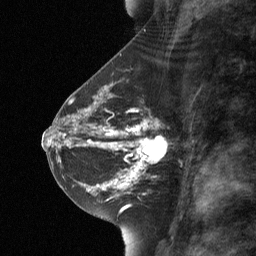
Breast MRI (dynamic contrast-enhanced), one sagittal slice; slice 32 of 64 in the series (ordered by position); dynamic contrast-enhanced study with each time point stored as its own series, time point 2 of 3 at this slice position (early post-contrast, ordered by acquisition time); 1.5 T; TE 4.8 ms, TR 27 ms; 2 mm slice thickness; 256 × 256 image matrix, field of view 180 × 180 mm. Patient: female, 42 years. Case-level facts recorded for this patient, not image findings: setting: breast cancer imaged before/during neoadjuvant chemotherapy; receptor status: triple-negative.
Outlined on this slice (semi-automatic segmentation, software-assisted and operator-edited):
- analysis volume of interest (the breast-tissue region the enhancement analysis was run in; not a lesion): bounding box (x1, y1, x2, y2) in pixels: (111, 128, 165, 178)
- tumour enhancement mask (voxels above the 90 % enhancement threshold inside the analysis volume of interest): (111, 131, 160, 178)